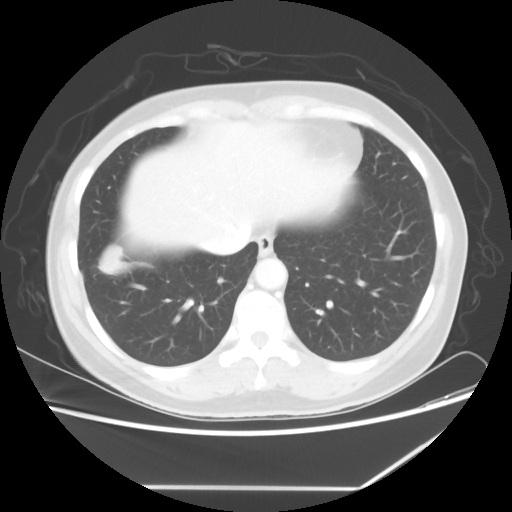
Chest CT, one axial slice; slice 18 of 60 in the series (ordered by position); lung window (W 1500 / L -600 HU); 5 mm slice thickness; 512 × 512 image matrix, field of view 374 × 374 mm. Female patient, age 42 years. Case-level facts recorded for this patient, not image findings: clinical TNM (as recorded): T2 N1 M0.
Annotated regions visible in this slice (bounding box drawn by a radiologist):
- lung tumour (recorded histology: adenocarcinoma): bounding box (x1, y1, x2, y2) in pixels: (97, 245, 128, 280)